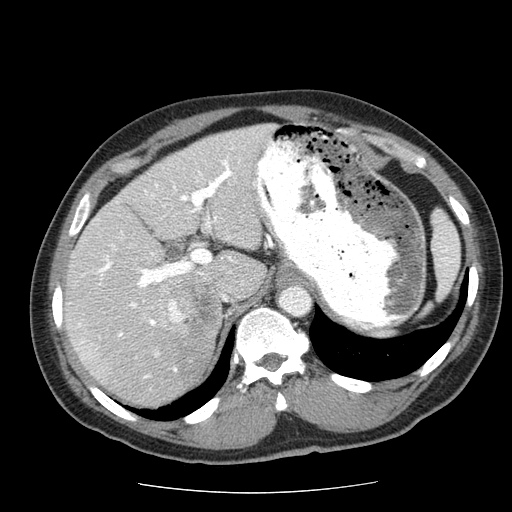
Contrast-enhanced abdominal CT (liver protocol), one axial slice; slice 41 of 85 in the series (ordered by position); reconstruction kernel STANDARD; soft-tissue window (W 400 / L 40 HU); 2.5 mm slice thickness; 512 × 512 image matrix. Case-level facts recorded for this patient, not image findings: diagnosis: hepatocellular carcinoma (patient treated with transarterial chemoembolisation; whether this scan precedes or follows treatment is not stated here); TNM stage (as recorded): Stage-IIIA; Child-Pugh class: A; tumour differentiation: well differentiated; tumour nodularity: multinodular.
Outlined on this slice (semi-automatic segmentation, software-assisted and operator-edited):
- abdominal aorta: bounding box [x1, y1, x2, y2] px = [278, 285, 311, 316]
- liver parenchyma outside the tumour (the mass and vessels are separate outlines, so this box may not span the whole liver): [64, 124, 274, 406]
- mass: [167, 280, 221, 338]
- liver vessels: [69, 148, 240, 378]